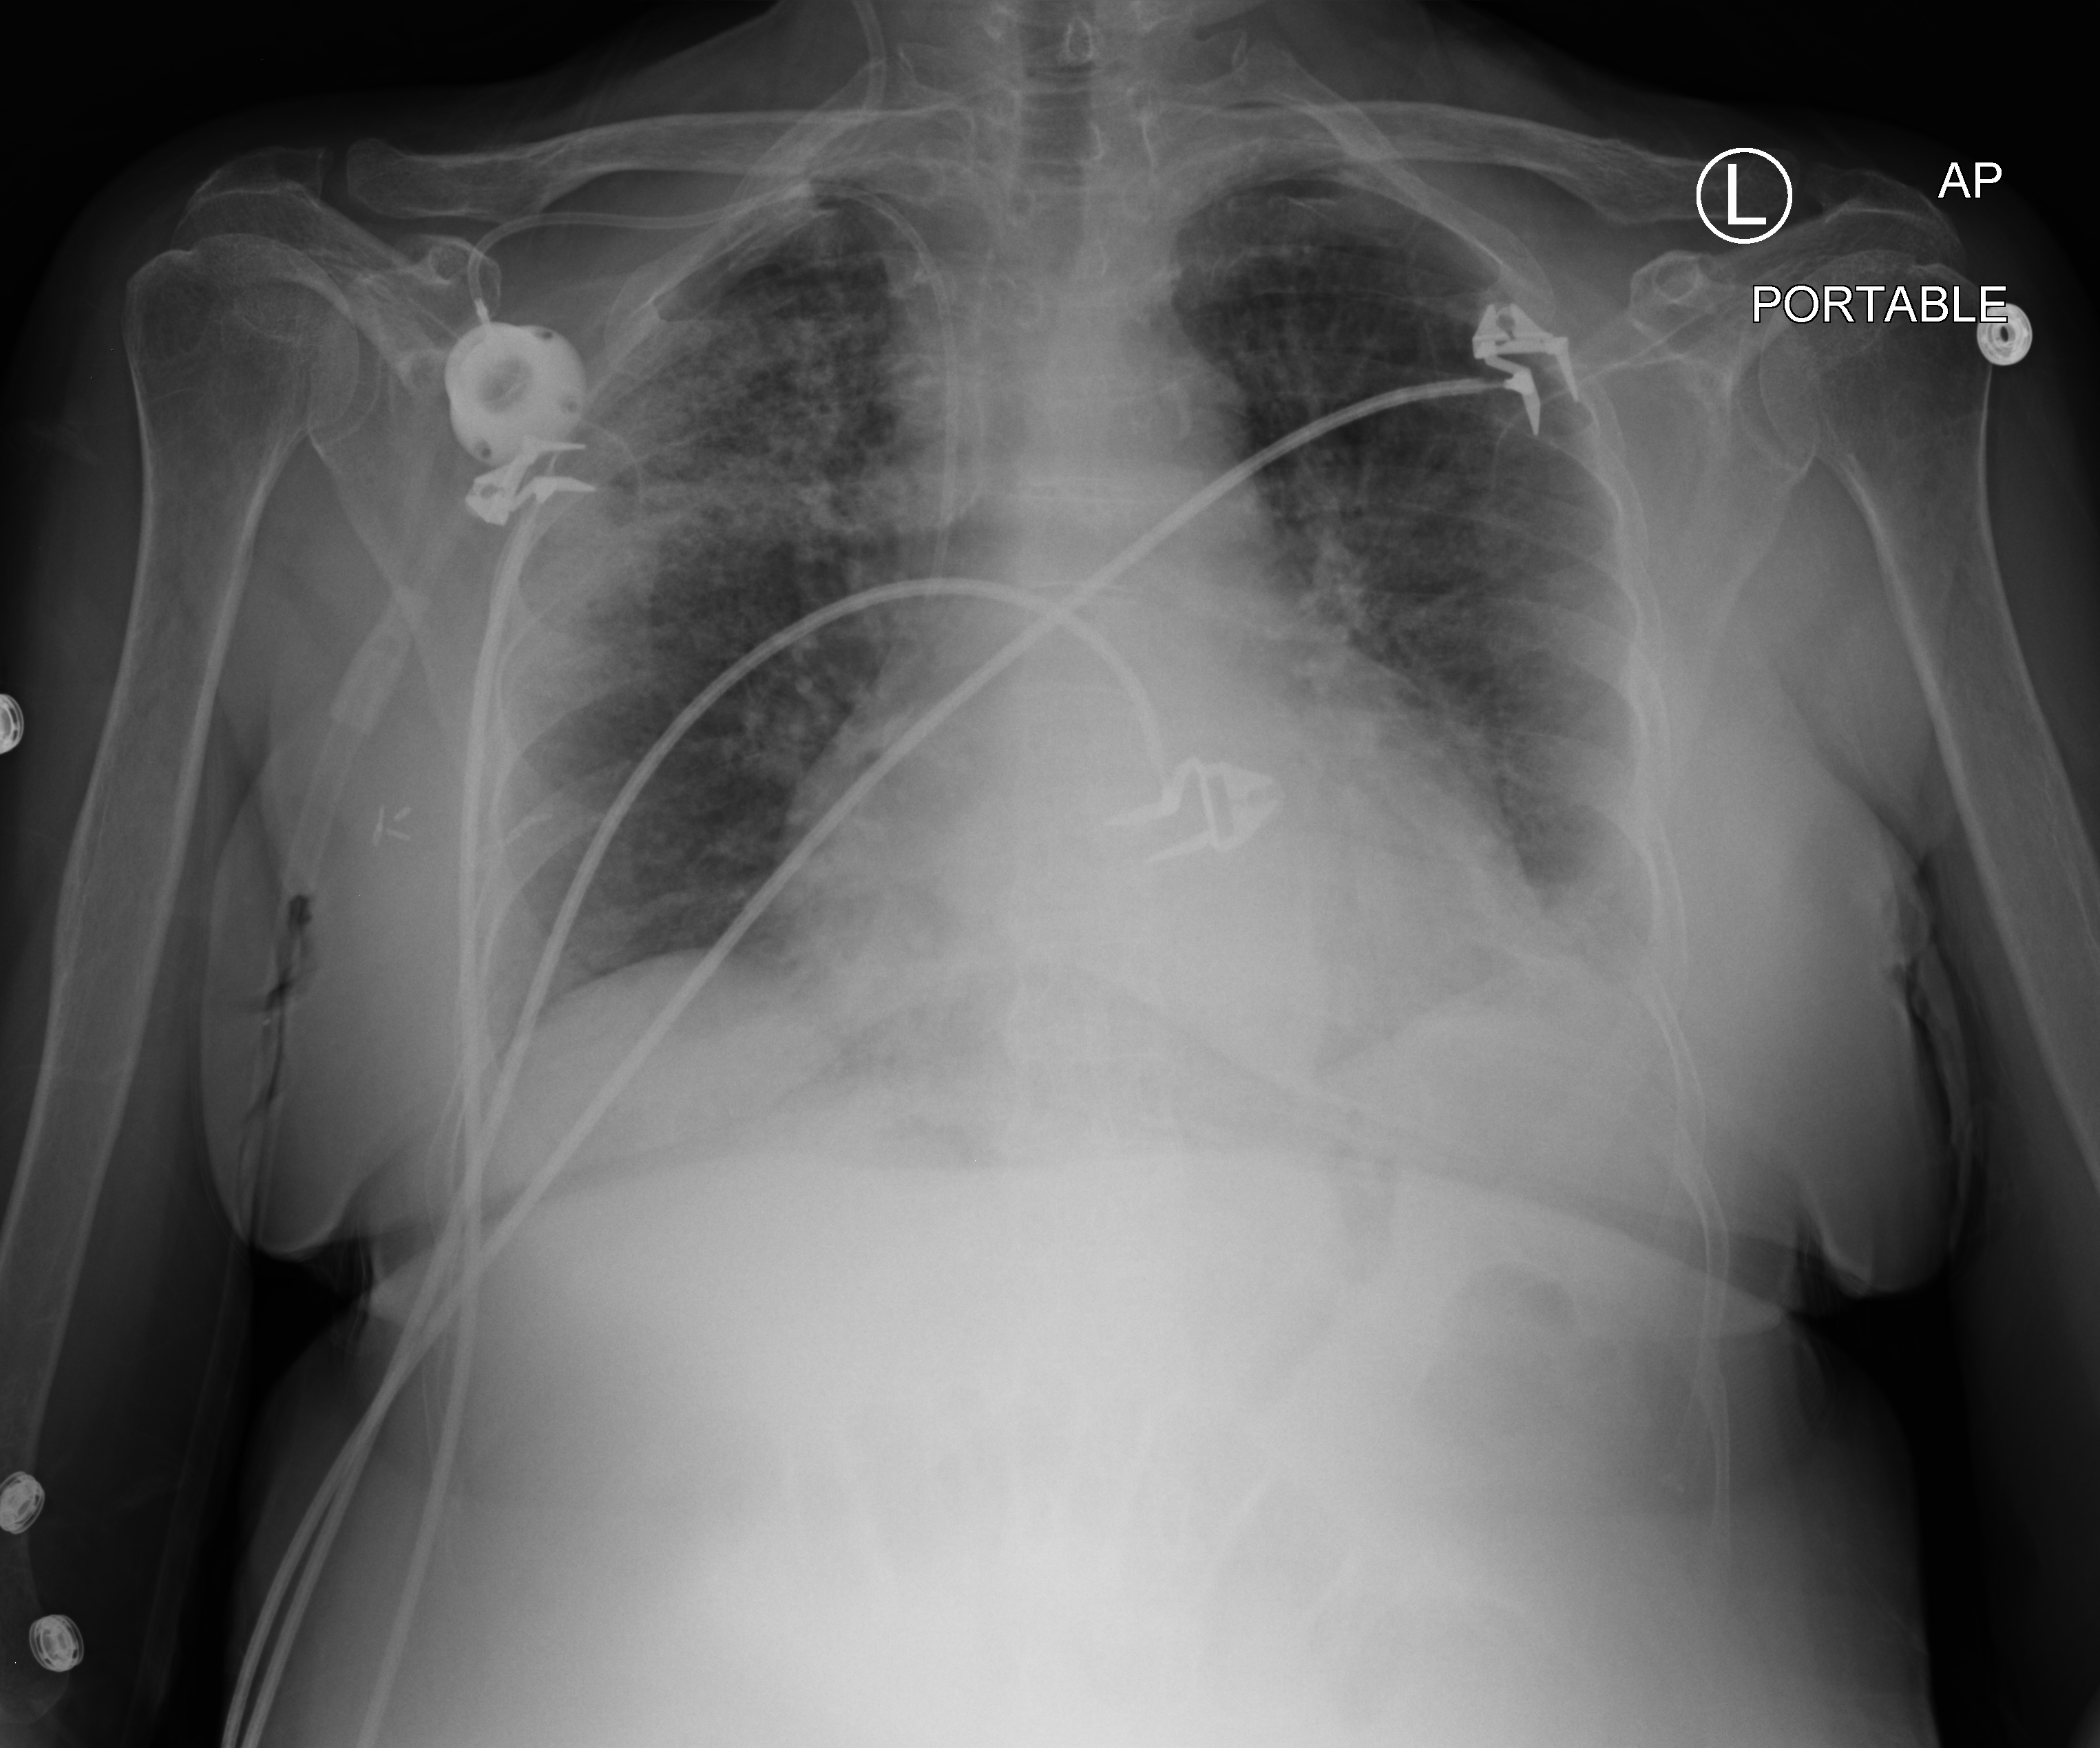
Portable chest radiograph. Patient hospitalised with COVID-19; female, aged 60–74 years.
Hospital-stay facts (about this admission, not read from this image; timing relative to this image not recorded): hypertension (admission record): yes; admitted to intensive care during this hospital stay: yes.